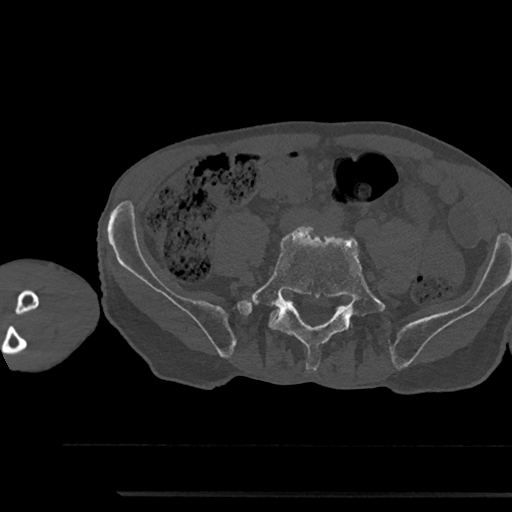
CT including the spine, one axial slice; slice 347 of 797 in the series (ordered by position); bone window (W 1800 / L 400 HU); 0.5 mm slice thickness; 512 × 512 image matrix, field of view 367 × 367 mm. Patient: male, 79 years. Case-level facts recorded for this patient, not image findings: primary cancer: prostate.
Structures marked on this image (semi-automatic segmentation, software-assisted and operator-edited):
- L5 vertebra: bounding box <244,227,386,370> (left, top, right, bottom; pixels)